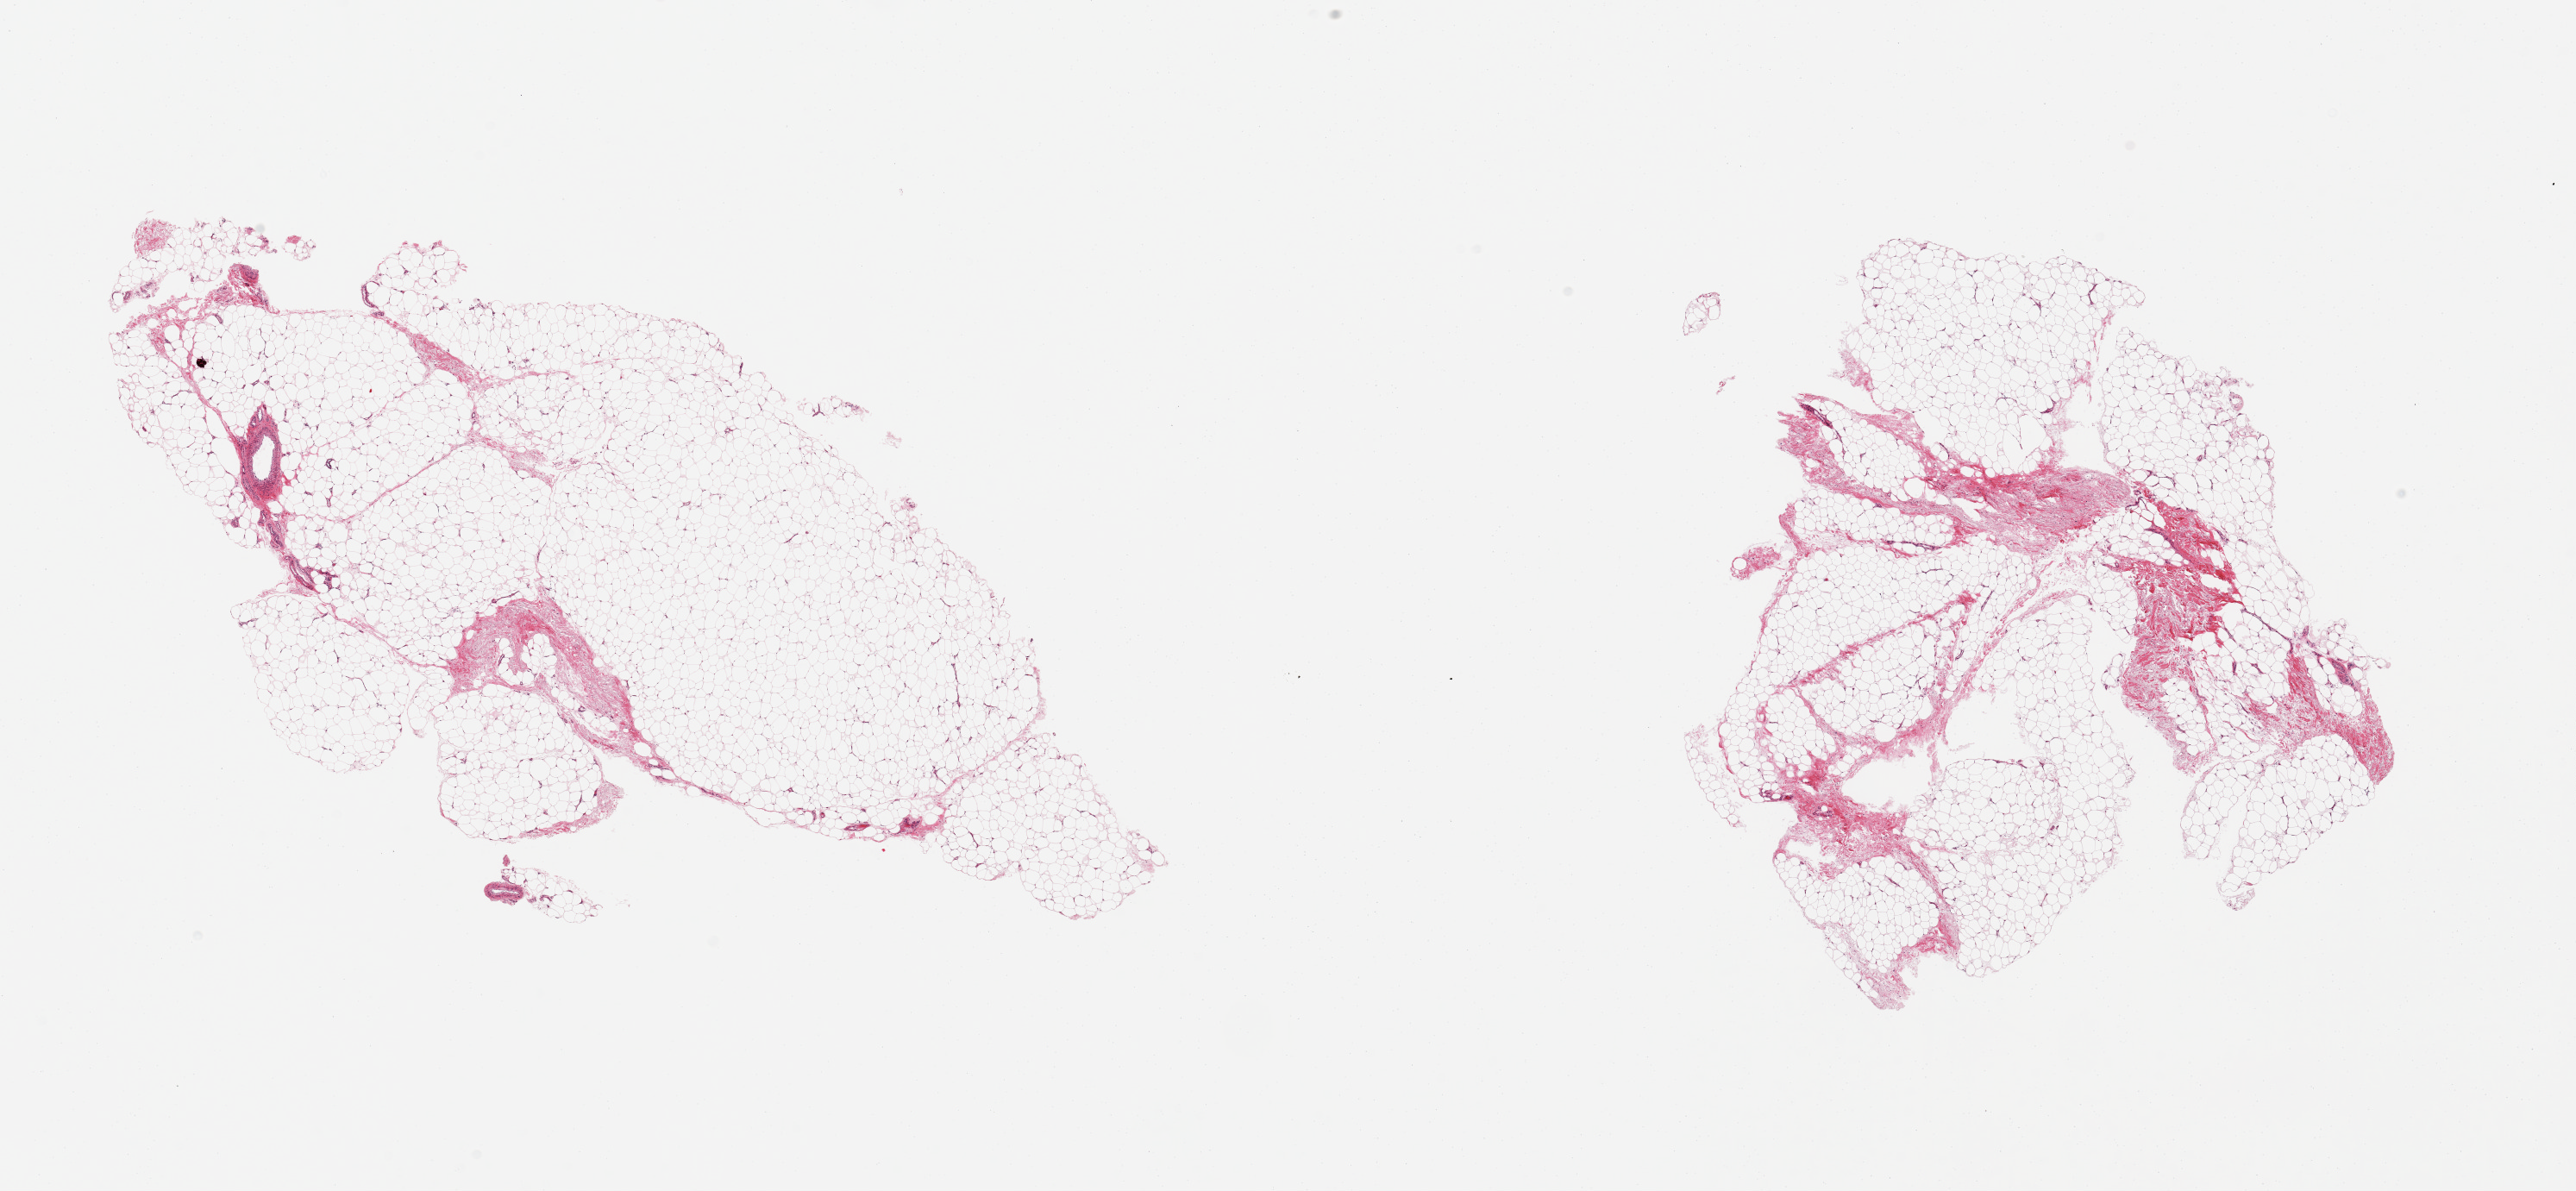
H&E whole-slide image, brightfield, low-resolution overview of the scanned area, about 23.6 x 10.9 mm, PAXgene-fixed paraffin-embedded (PFPE) section, section of adipose tissue (target tissue), donor tissue sample. Male donor.
Review note (as recorded): 2 pieces.